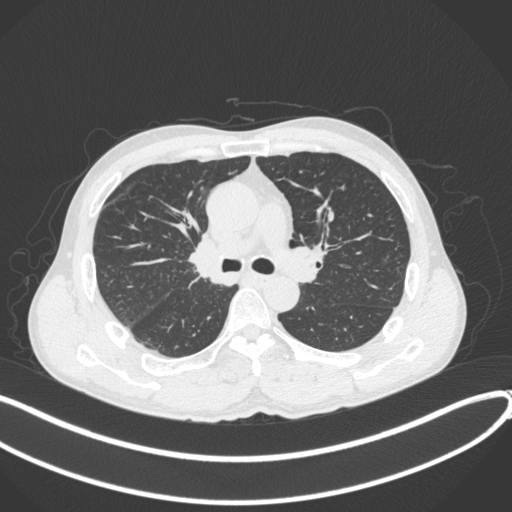
Chest CT, one axial slice. Slice 240 of 409 in the series (ordered by position). Lung window (W 1500 / L -600 HU). 1 mm slice thickness. 512 × 512 image matrix, field of view 400 × 400 mm. Patient: male, 53 years. From the clinical record (not read from this slice): clinical TNM (as recorded): T1b N0 M0.
Structures marked on this image (rectangle marked by the reading radiologist):
- lung tumour (recorded histology: squamous cell carcinoma): bounding box (x1, y1, x2, y2) in pixels: (176, 228, 221, 284)